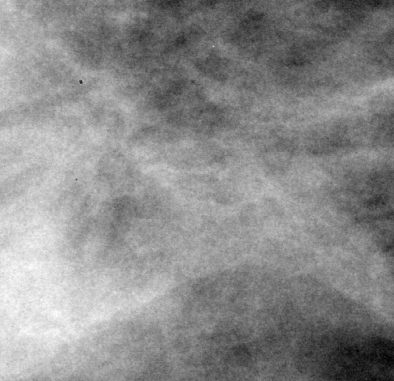
Region of interest cut from a scanned film mammogram (one marked finding); right breast; CC view.
Finding: mass, shape architectural distortion; BI-RADS assessment category 4; subtlety rating 4 on a 1 (subtle) to 5 (obvious) scale; benign; no additional work-up was recommended (benign without callback).